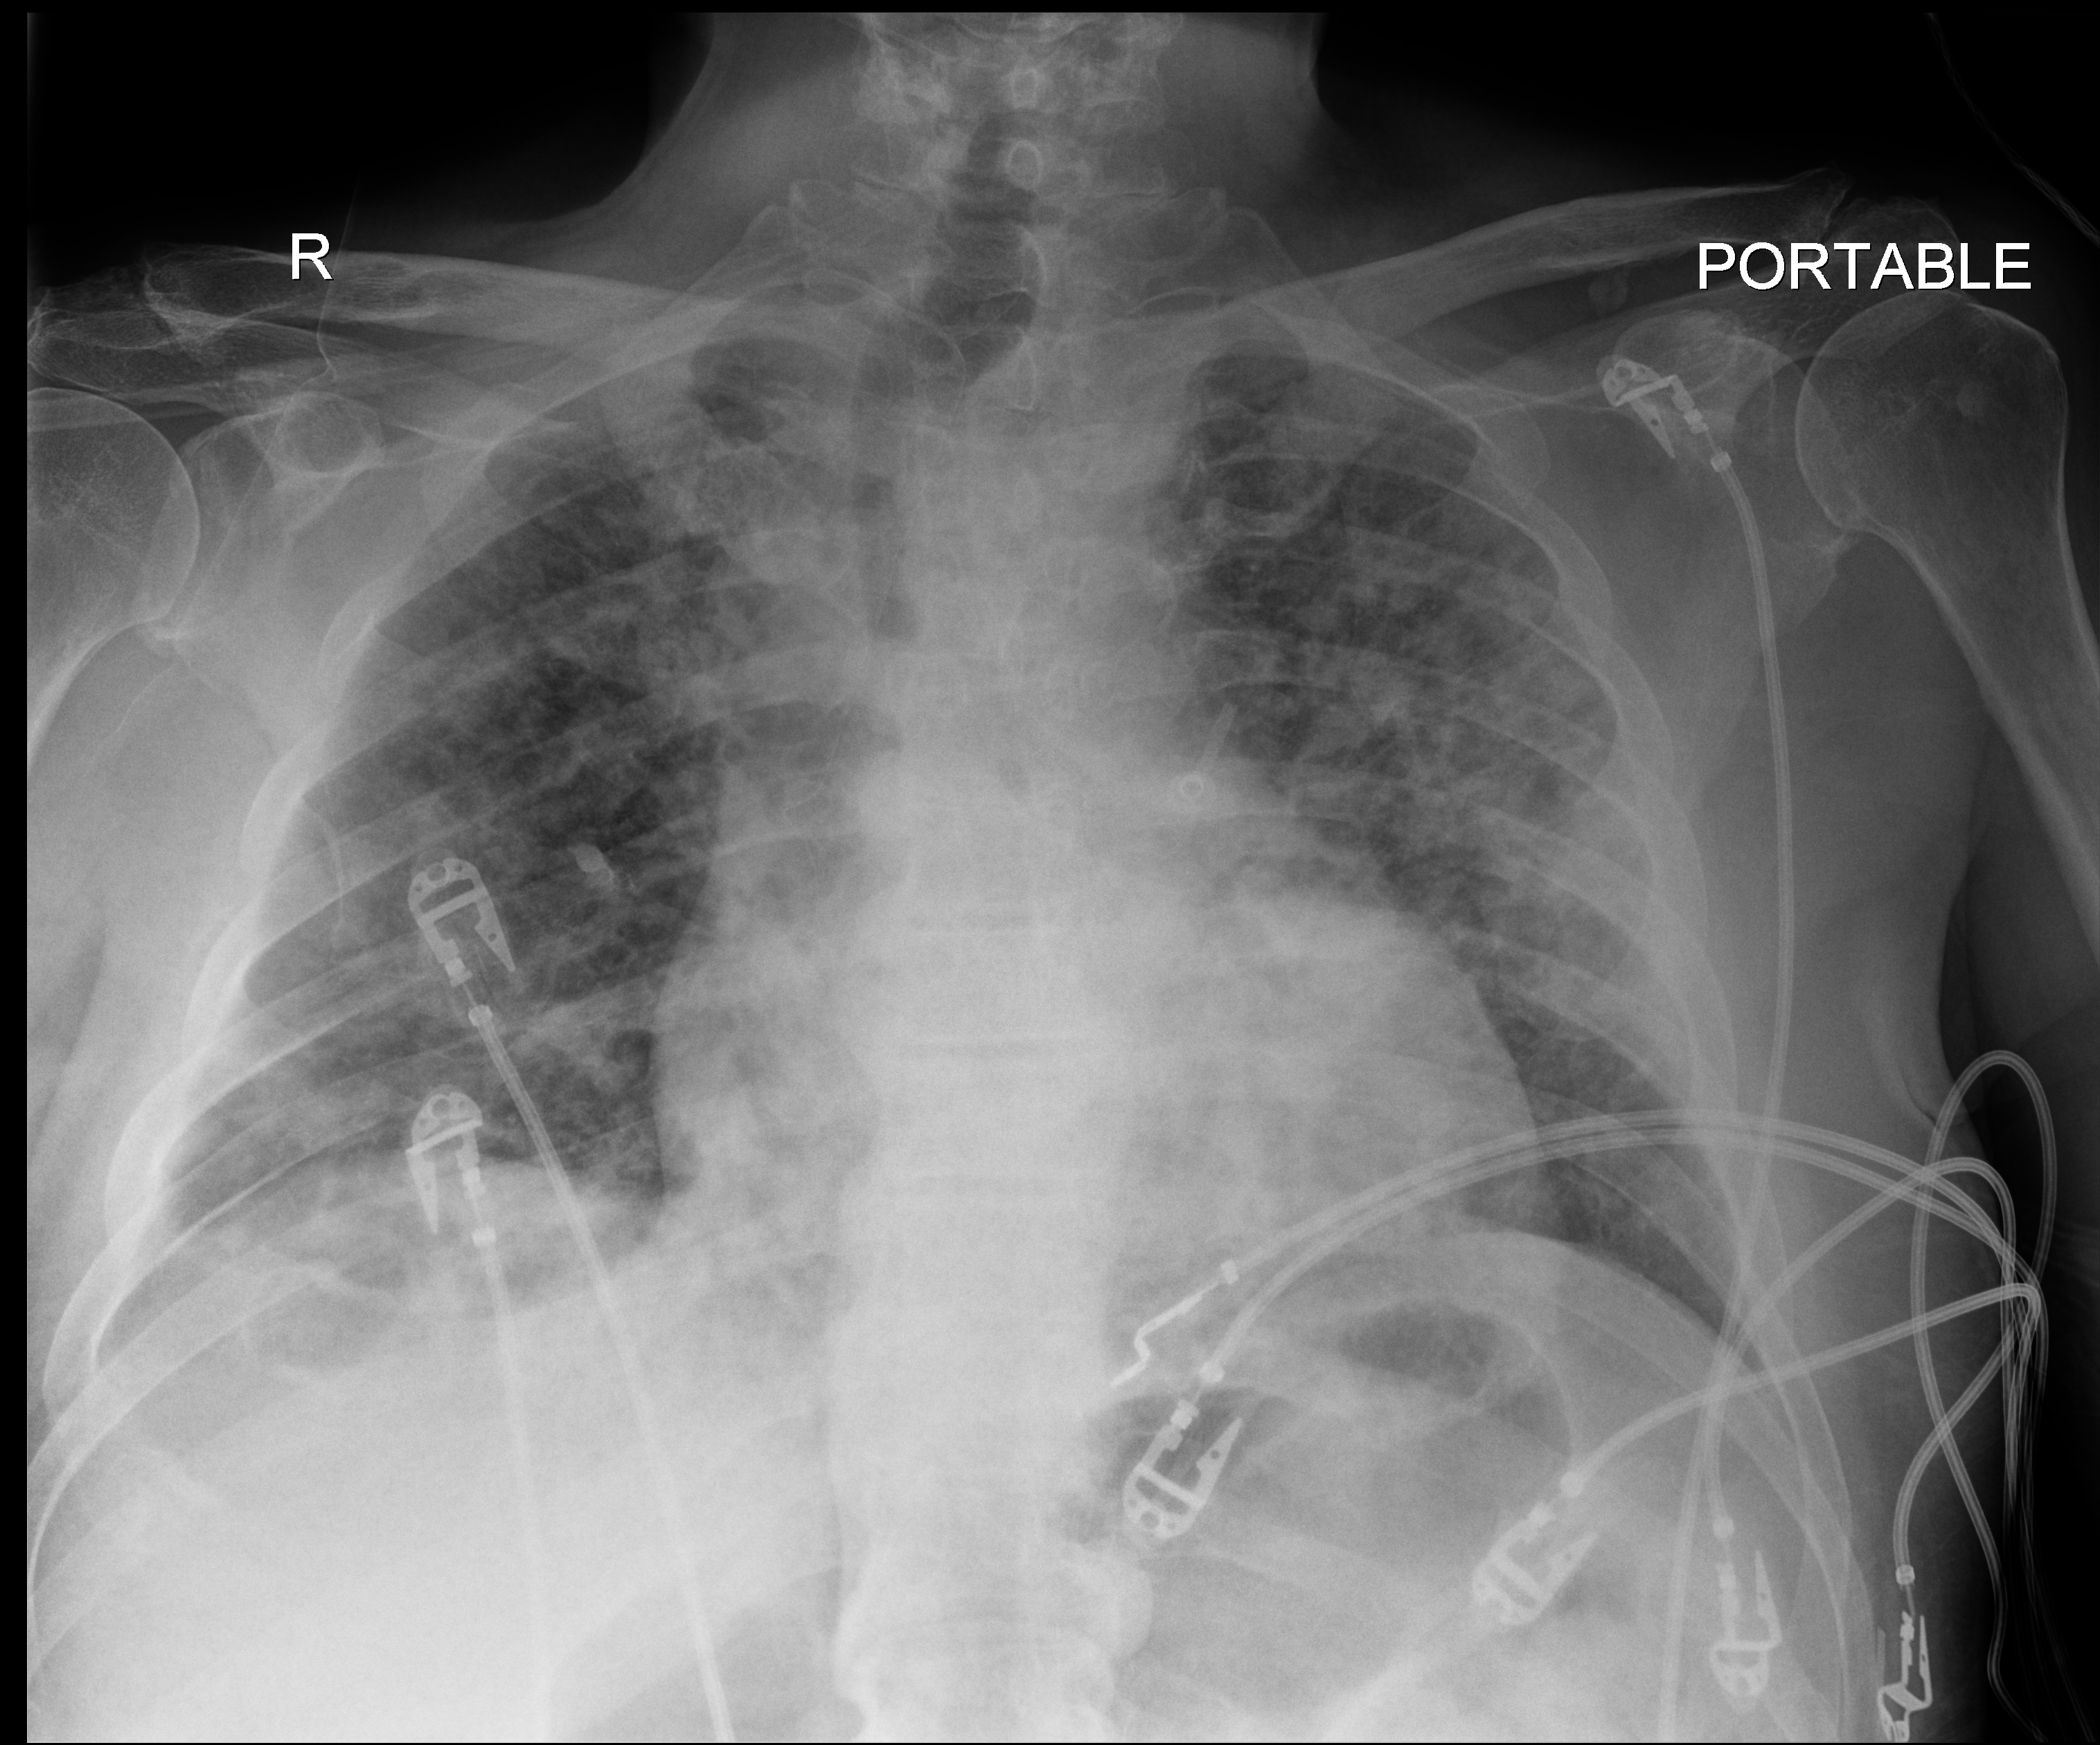
Chest radiograph (digital radiography). Patient hospitalised with COVID-19; male, aged 18–59 years.
From the hospital-stay record, not from the radiograph (when in the stay this image was taken is not recorded):
- hypertension (admission record): yes